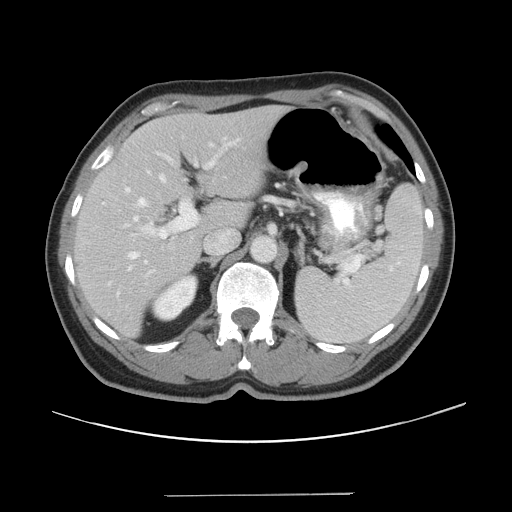
Contrast-enhanced abdominal CT, one axial slice. Position 26 of 43 along the scan axis. 120 kVp. Intravenous contrast given. Soft-tissue window (W 400 / L 40 HU). 5 mm slice thickness. 512 × 512 image matrix. Male patient, age 65 years. Case-level facts recorded for this patient, not image findings: diagnosis: colorectal cancer liver metastases, imaged before liver resection; multiple liver metastases: no; largest metastasis: 3.8 cm.
Annotated regions visible in this slice (outlined manually by an expert reader):
- hepatic veins: bounding box <109,169,167,285> (left, top, right, bottom; pixels)
- liver: <75,108,278,335>
- planned liver remnant (the part of the liver to remain after resection): <75,108,278,335>
- portal vein (with intrahepatic branches): <125,137,245,277>